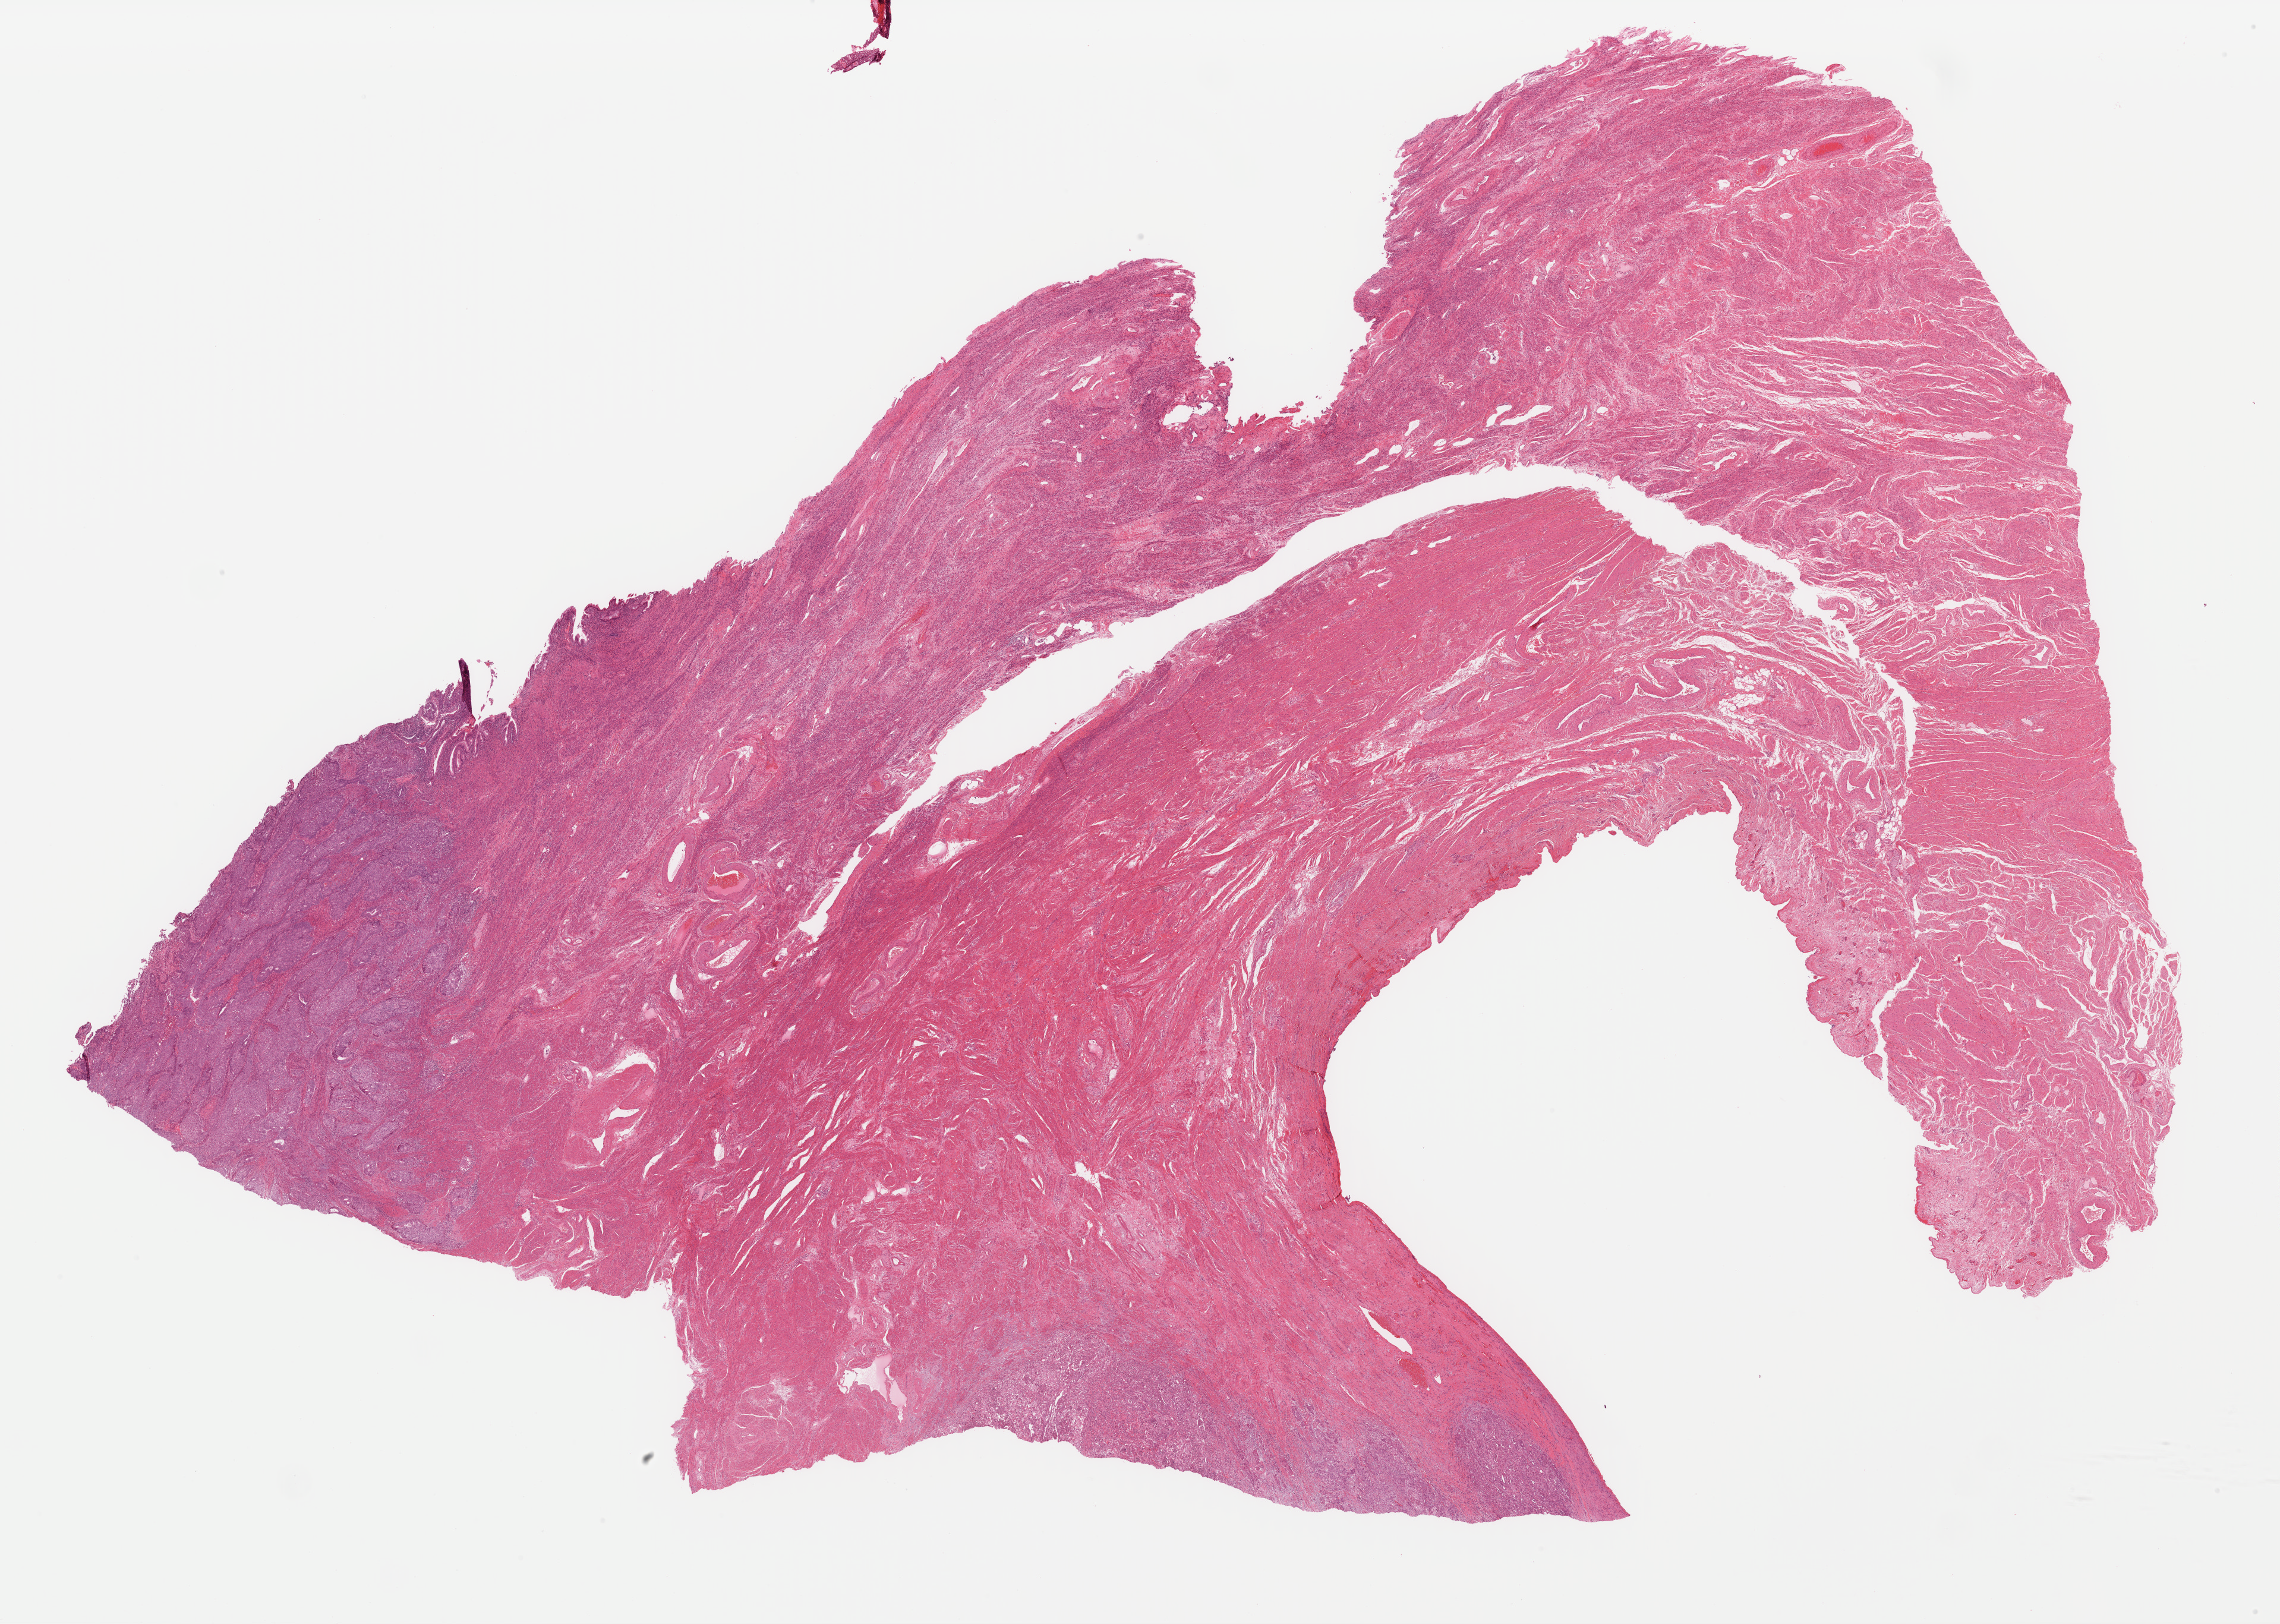
Whole-slide histology image, H&E, shown as a low-resolution overview of the whole scanned area (about 30.3 x 21.6 mm). Formalin-fixed paraffin-embedded (FFPE) diagnostic section. Primary tumour sample from the uterus. Female patient; age at initial diagnosis 81 years. Histologic grade: G3 (poorly differentiated).
Pathologic diagnosis: Endometrioid adenocarcinoma, NOS (endometrium). Lymph nodes positive (case pathology): 0 of 4 examined. FIGO stage: IIIC.